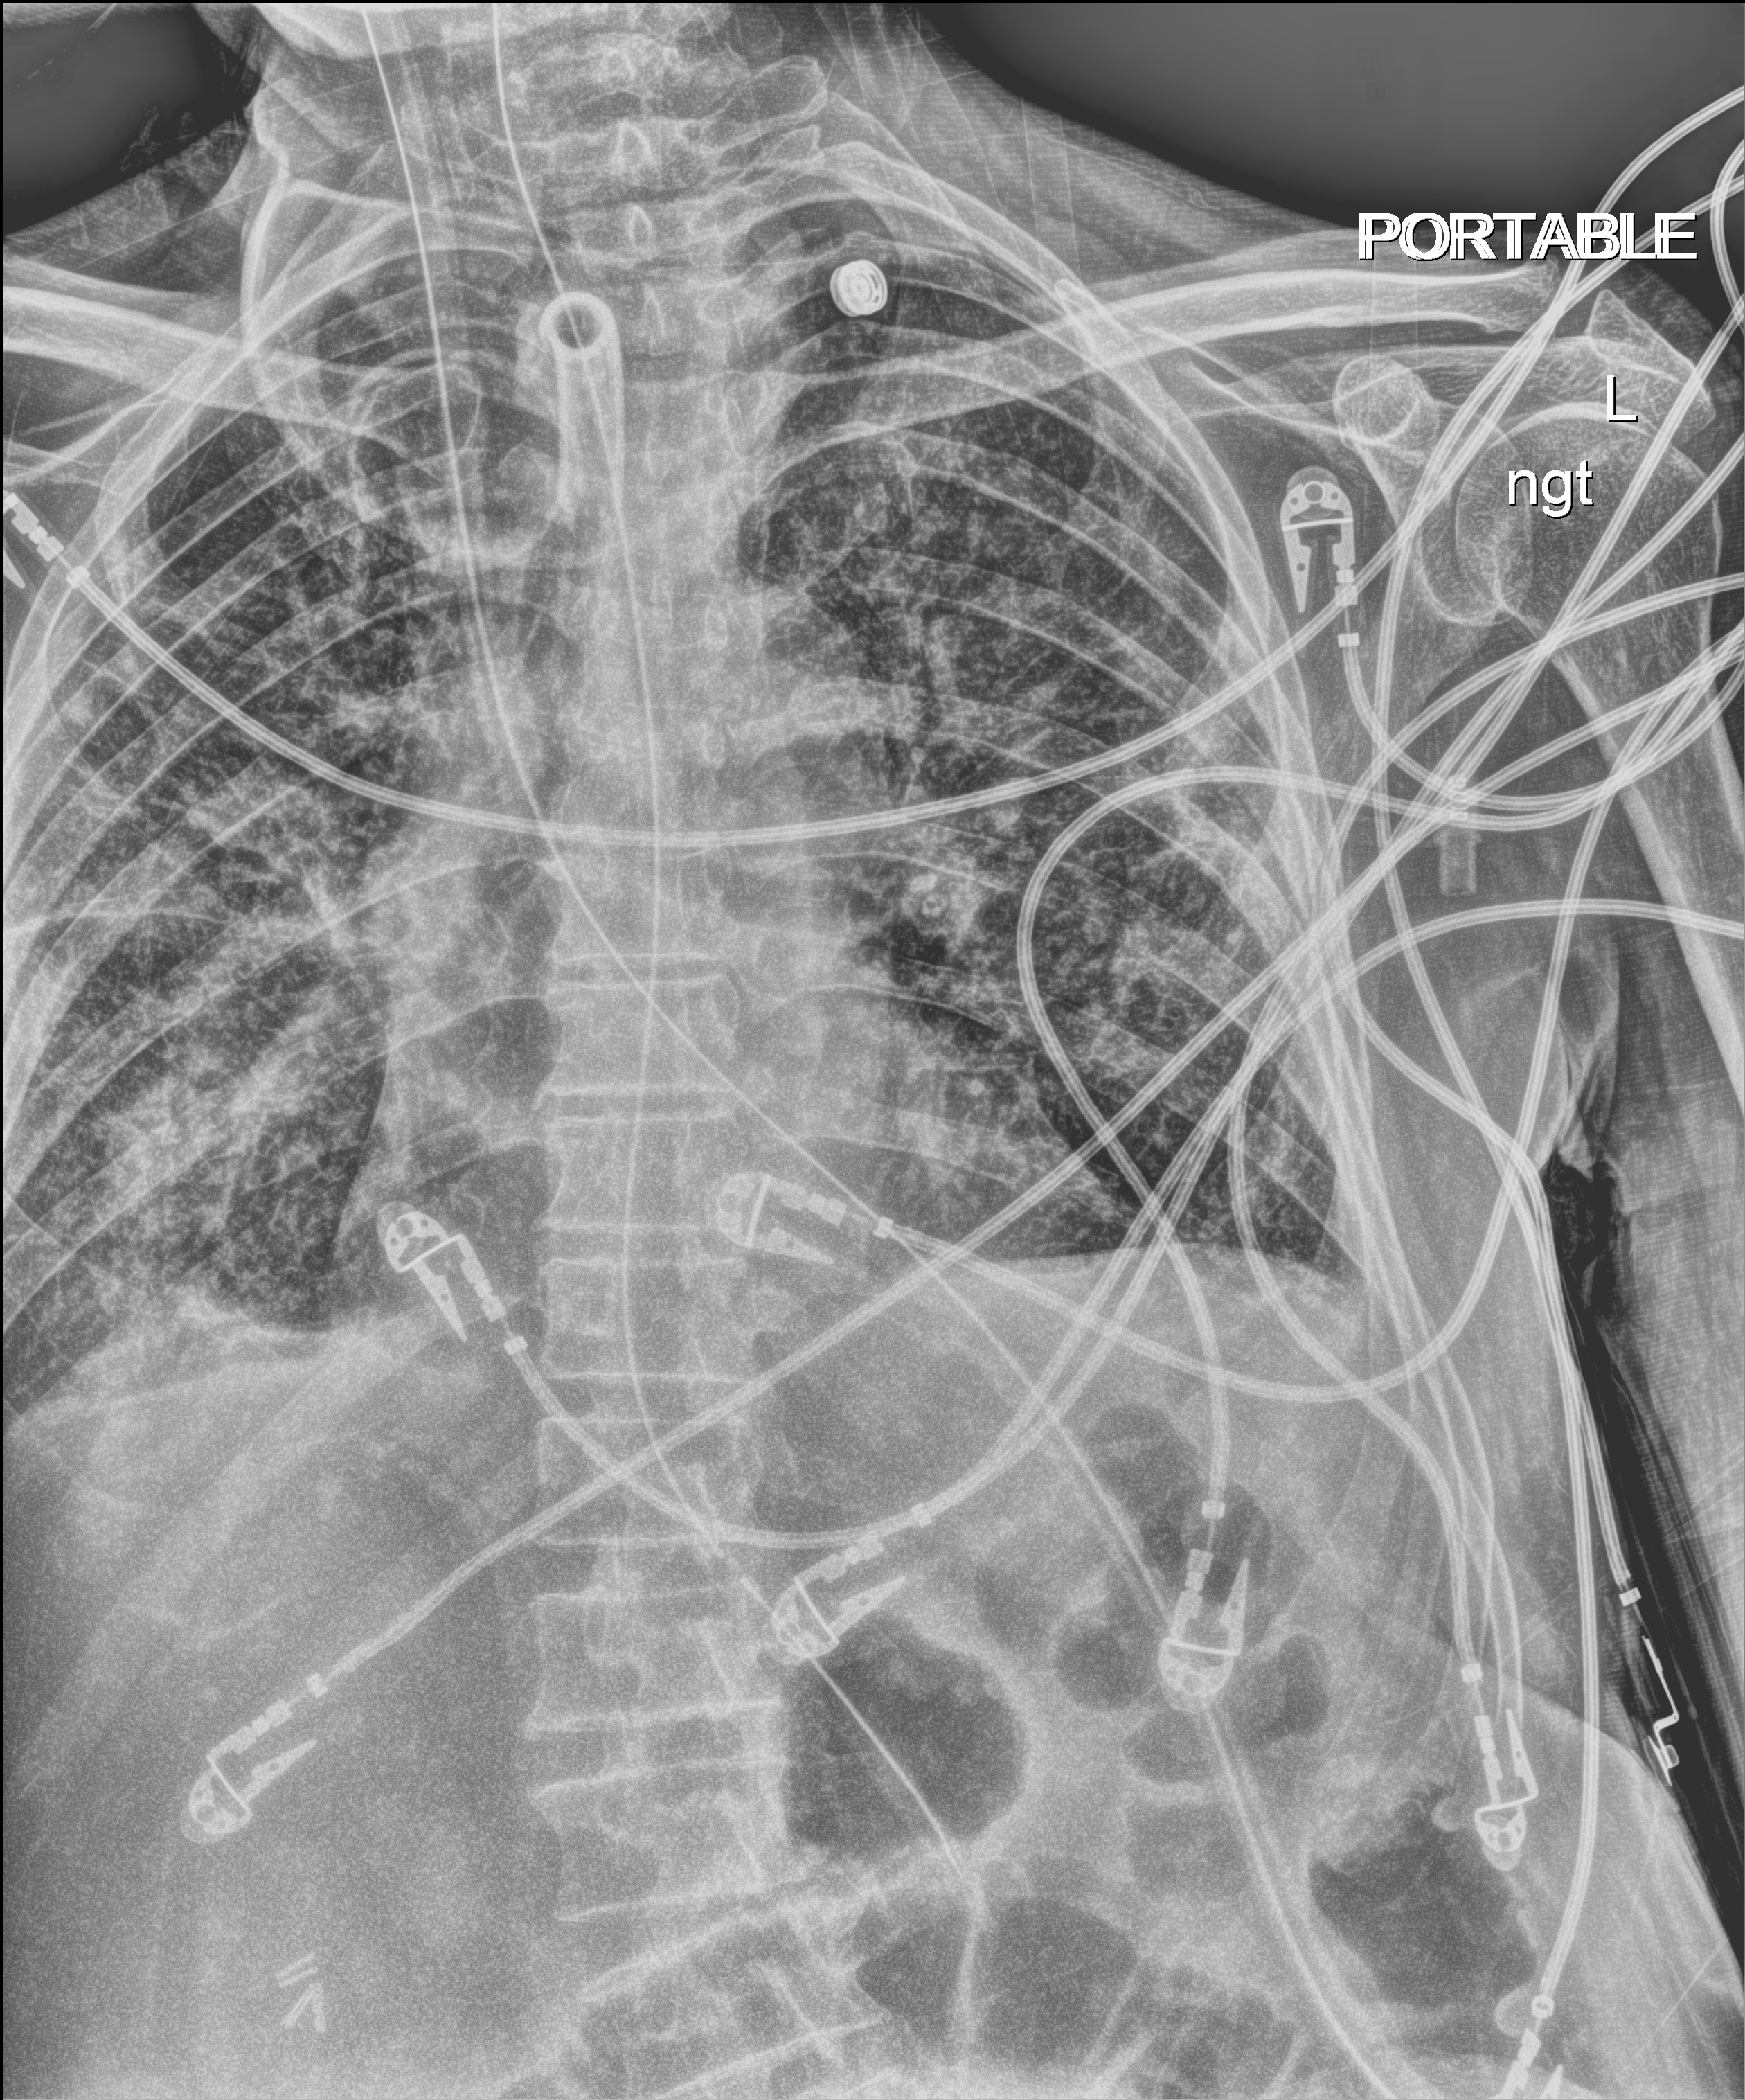
Bedside chest radiograph (digital radiography). Patient hospitalised with COVID-19; male, aged 75–90 years.
From the hospital-stay record, not from the radiograph (when in the stay this image was taken is not recorded):
- length of hospital stay: 70 days
- other chronic lung disease (admission record): yes
- admitted to intensive care during this hospital stay: yes